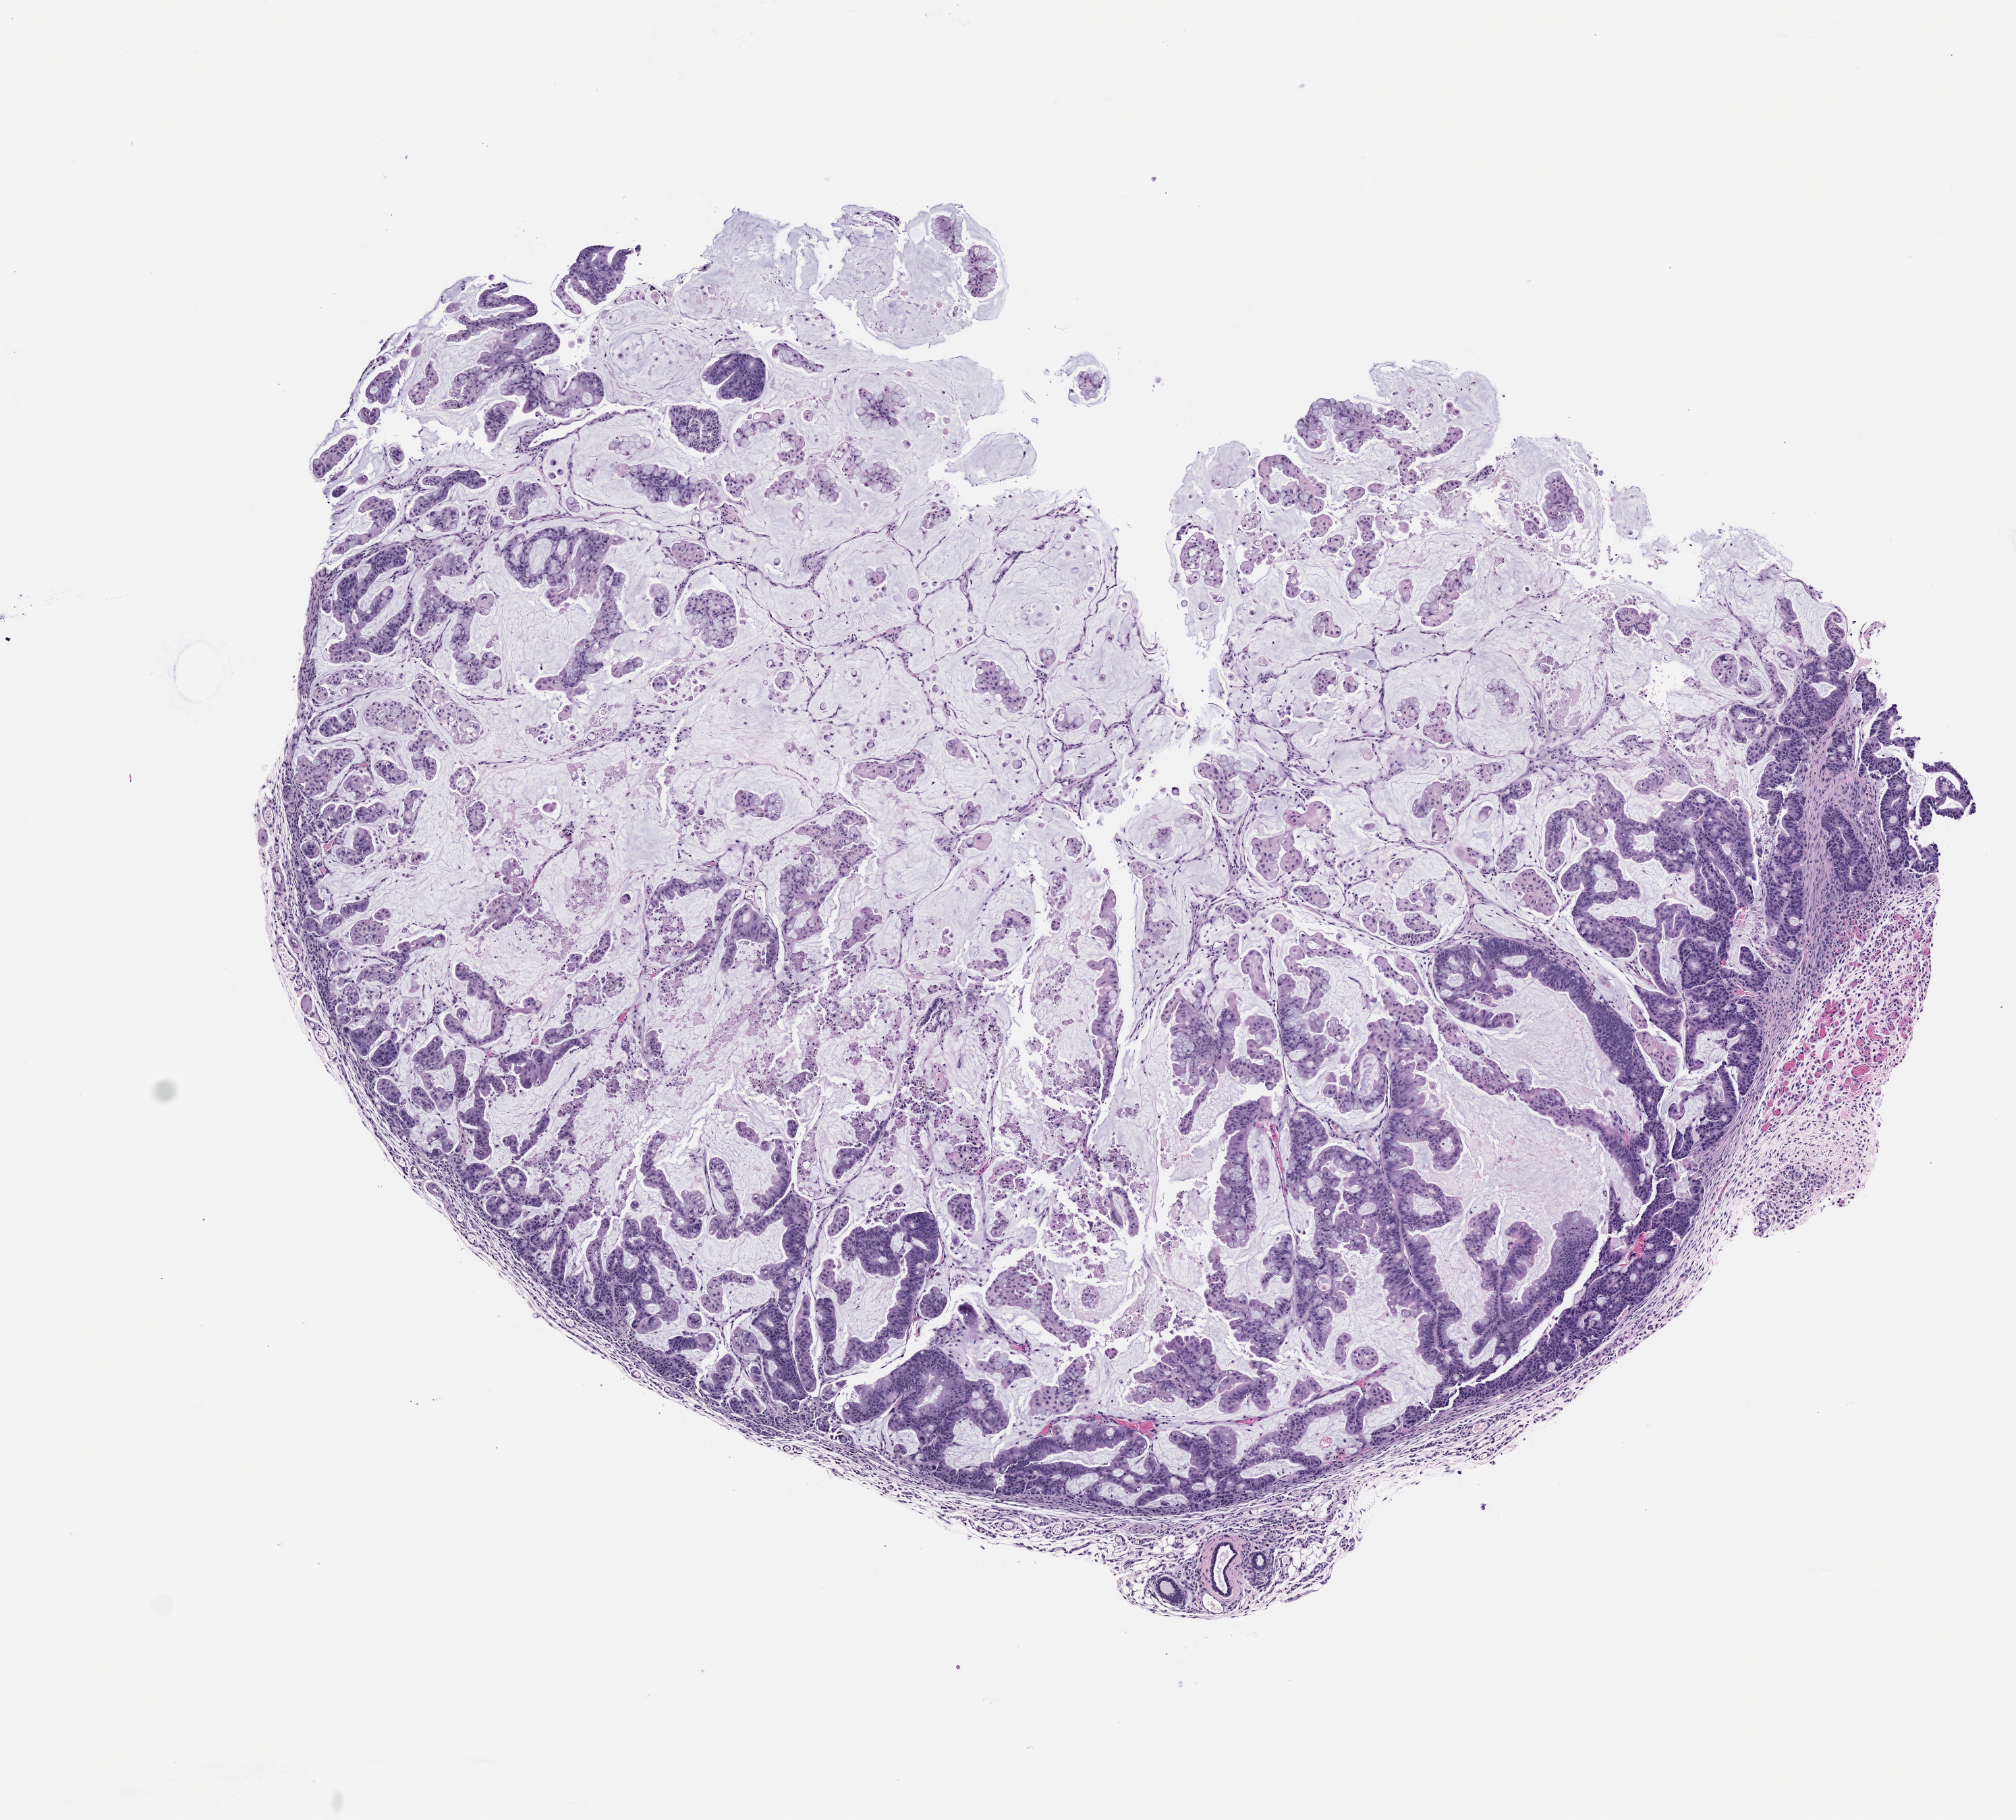
Hematoxylin and eosin (H&E) whole-slide image of a patient-derived xenograft (PDX) tumor grown in a mouse, passage 1 — shown as a low-resolution overview of the whole scanned area (about 6.0 x 5.4 mm). Formalin-fixed paraffin-embedded section. Tumor site category: colon.
Originating patient diagnosis: Colon Adenocarcinoma.